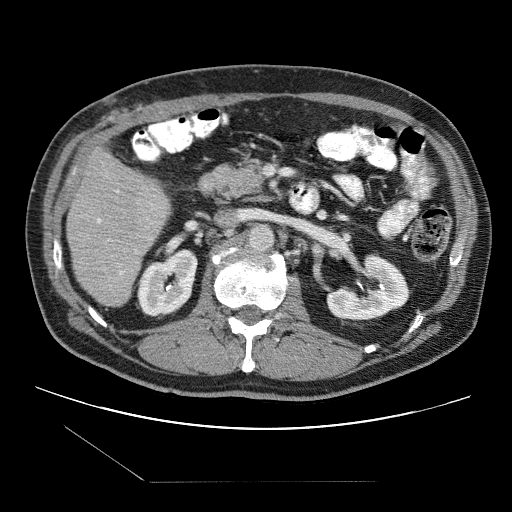
Contrast-enhanced abdominal CT (liver protocol), one axial slice. Position 36 of 109 along the scan axis. Reconstruction kernel STANDARD. One of 2 acquisitions stored at this slice position. Soft-tissue window (W 400 / L 40 HU). 2.5 mm slice thickness. 512 × 512 image matrix, field of view 400 × 400 mm. From the clinical record (not read from this slice): diagnosis: hepatocellular carcinoma (patient treated with transarterial chemoembolisation; whether this scan precedes or follows treatment is not stated here); TNM stage (as recorded): Stage-IIIB; Child-Pugh class: A; tumour differentiation: well differentiated; tumour nodularity: multinodular.
Structures marked on this image (semi-automatic segmentation, software-assisted and operator-edited):
- liver parenchyma outside the tumour (the mass and vessels are separate outlines, so this box may not span the whole liver): bounding box <66,148,170,306> (left, top, right, bottom; pixels)
- liver vessels: <97,191,137,275>